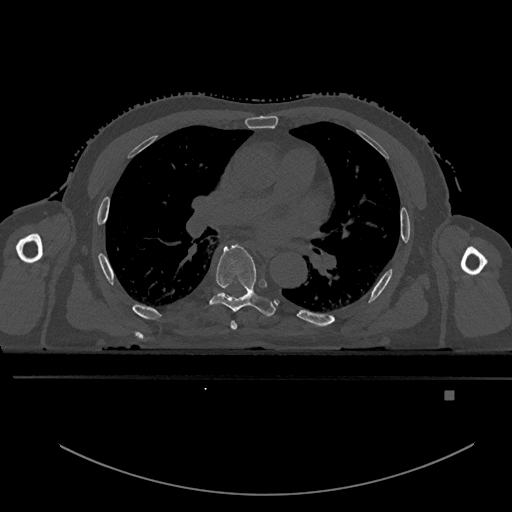
CT including the spine, one axial slice; position 310 of 969 along the scan axis; bone window (W 1800 / L 400 HU); 0.5 mm slice thickness; 512 × 512 image matrix, field of view 456 × 456 mm. Patient: male, 82 years. Case-level facts recorded for this patient, not image findings: primary cancer: prostate.
Annotated regions visible in this slice (semi-automatic segmentation, software-assisted and operator-edited):
- T5 vertebra: bounding box (x1, y1, x2, y2) in pixels: (230, 320, 237, 330)
- T6 vertebra: (200, 245, 277, 317)